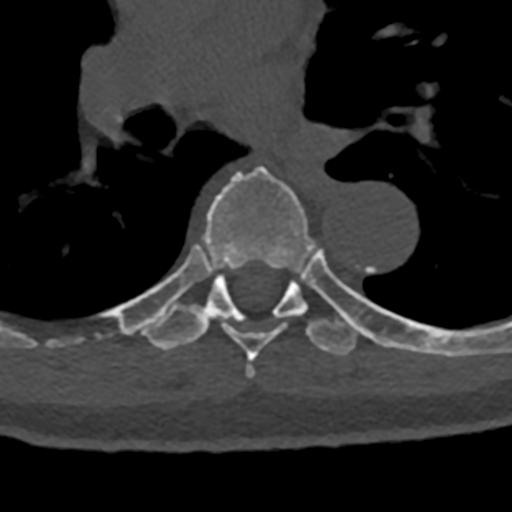
CT including the spine, one axial slice; position 788 of 797 along the scan axis; reconstruction kernel Br40s/3; 120 kVp; bone window (W 1800 / L 400 HU); 512 × 512 image matrix. Patient: male, 74 years. Case-level facts recorded for this patient, not image findings: primary cancer: renal.
Outlined on this slice (semi-automatic segmentation, software-assisted and operator-edited):
- T6 vertebra: bounding box (x1, y1, x2, y2) in pixels: (161, 165, 314, 378)
- T7 vertebra: (110, 247, 432, 357)